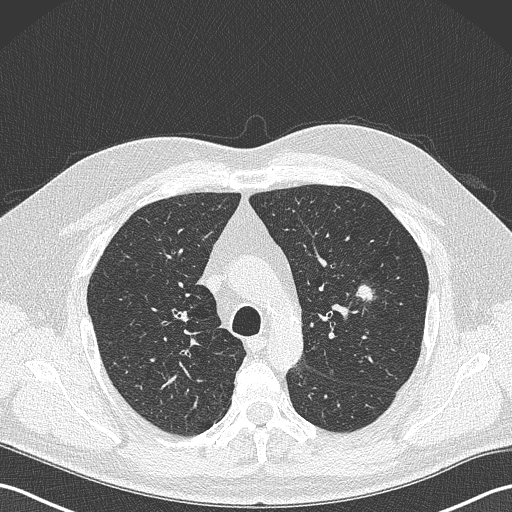
Axial slice from a low-dose chest CT screening exam. First (baseline) screen. Lung window (W 1500 / L -600 HU). 1 mm slice thickness. Slice 101 of 343 in the series. Male participant, aged 61 years at enrolment. Former smoker at enrolment.
Expert-annotated lung lesion, bounding box <339,274,386,317> (left, top, right, bottom; pixels). The screening reader recorded 2 non-calcified nodules or masses ≥4 mm on this exam; which of them this box marks is not recorded. Official screen result: positive, change unspecified: nodule(s) >= 4 mm or enlarging nodule(s), mass(es), or other non-specific abnormalities suspicious for lung cancer. Later outcome: lung cancer diagnosed 160 days after this screen — adenocarcinoma, NOS, left upper lobe, poorly differentiated (G3), stage IA (AJCC 6th edition), 28 mm at pathology.